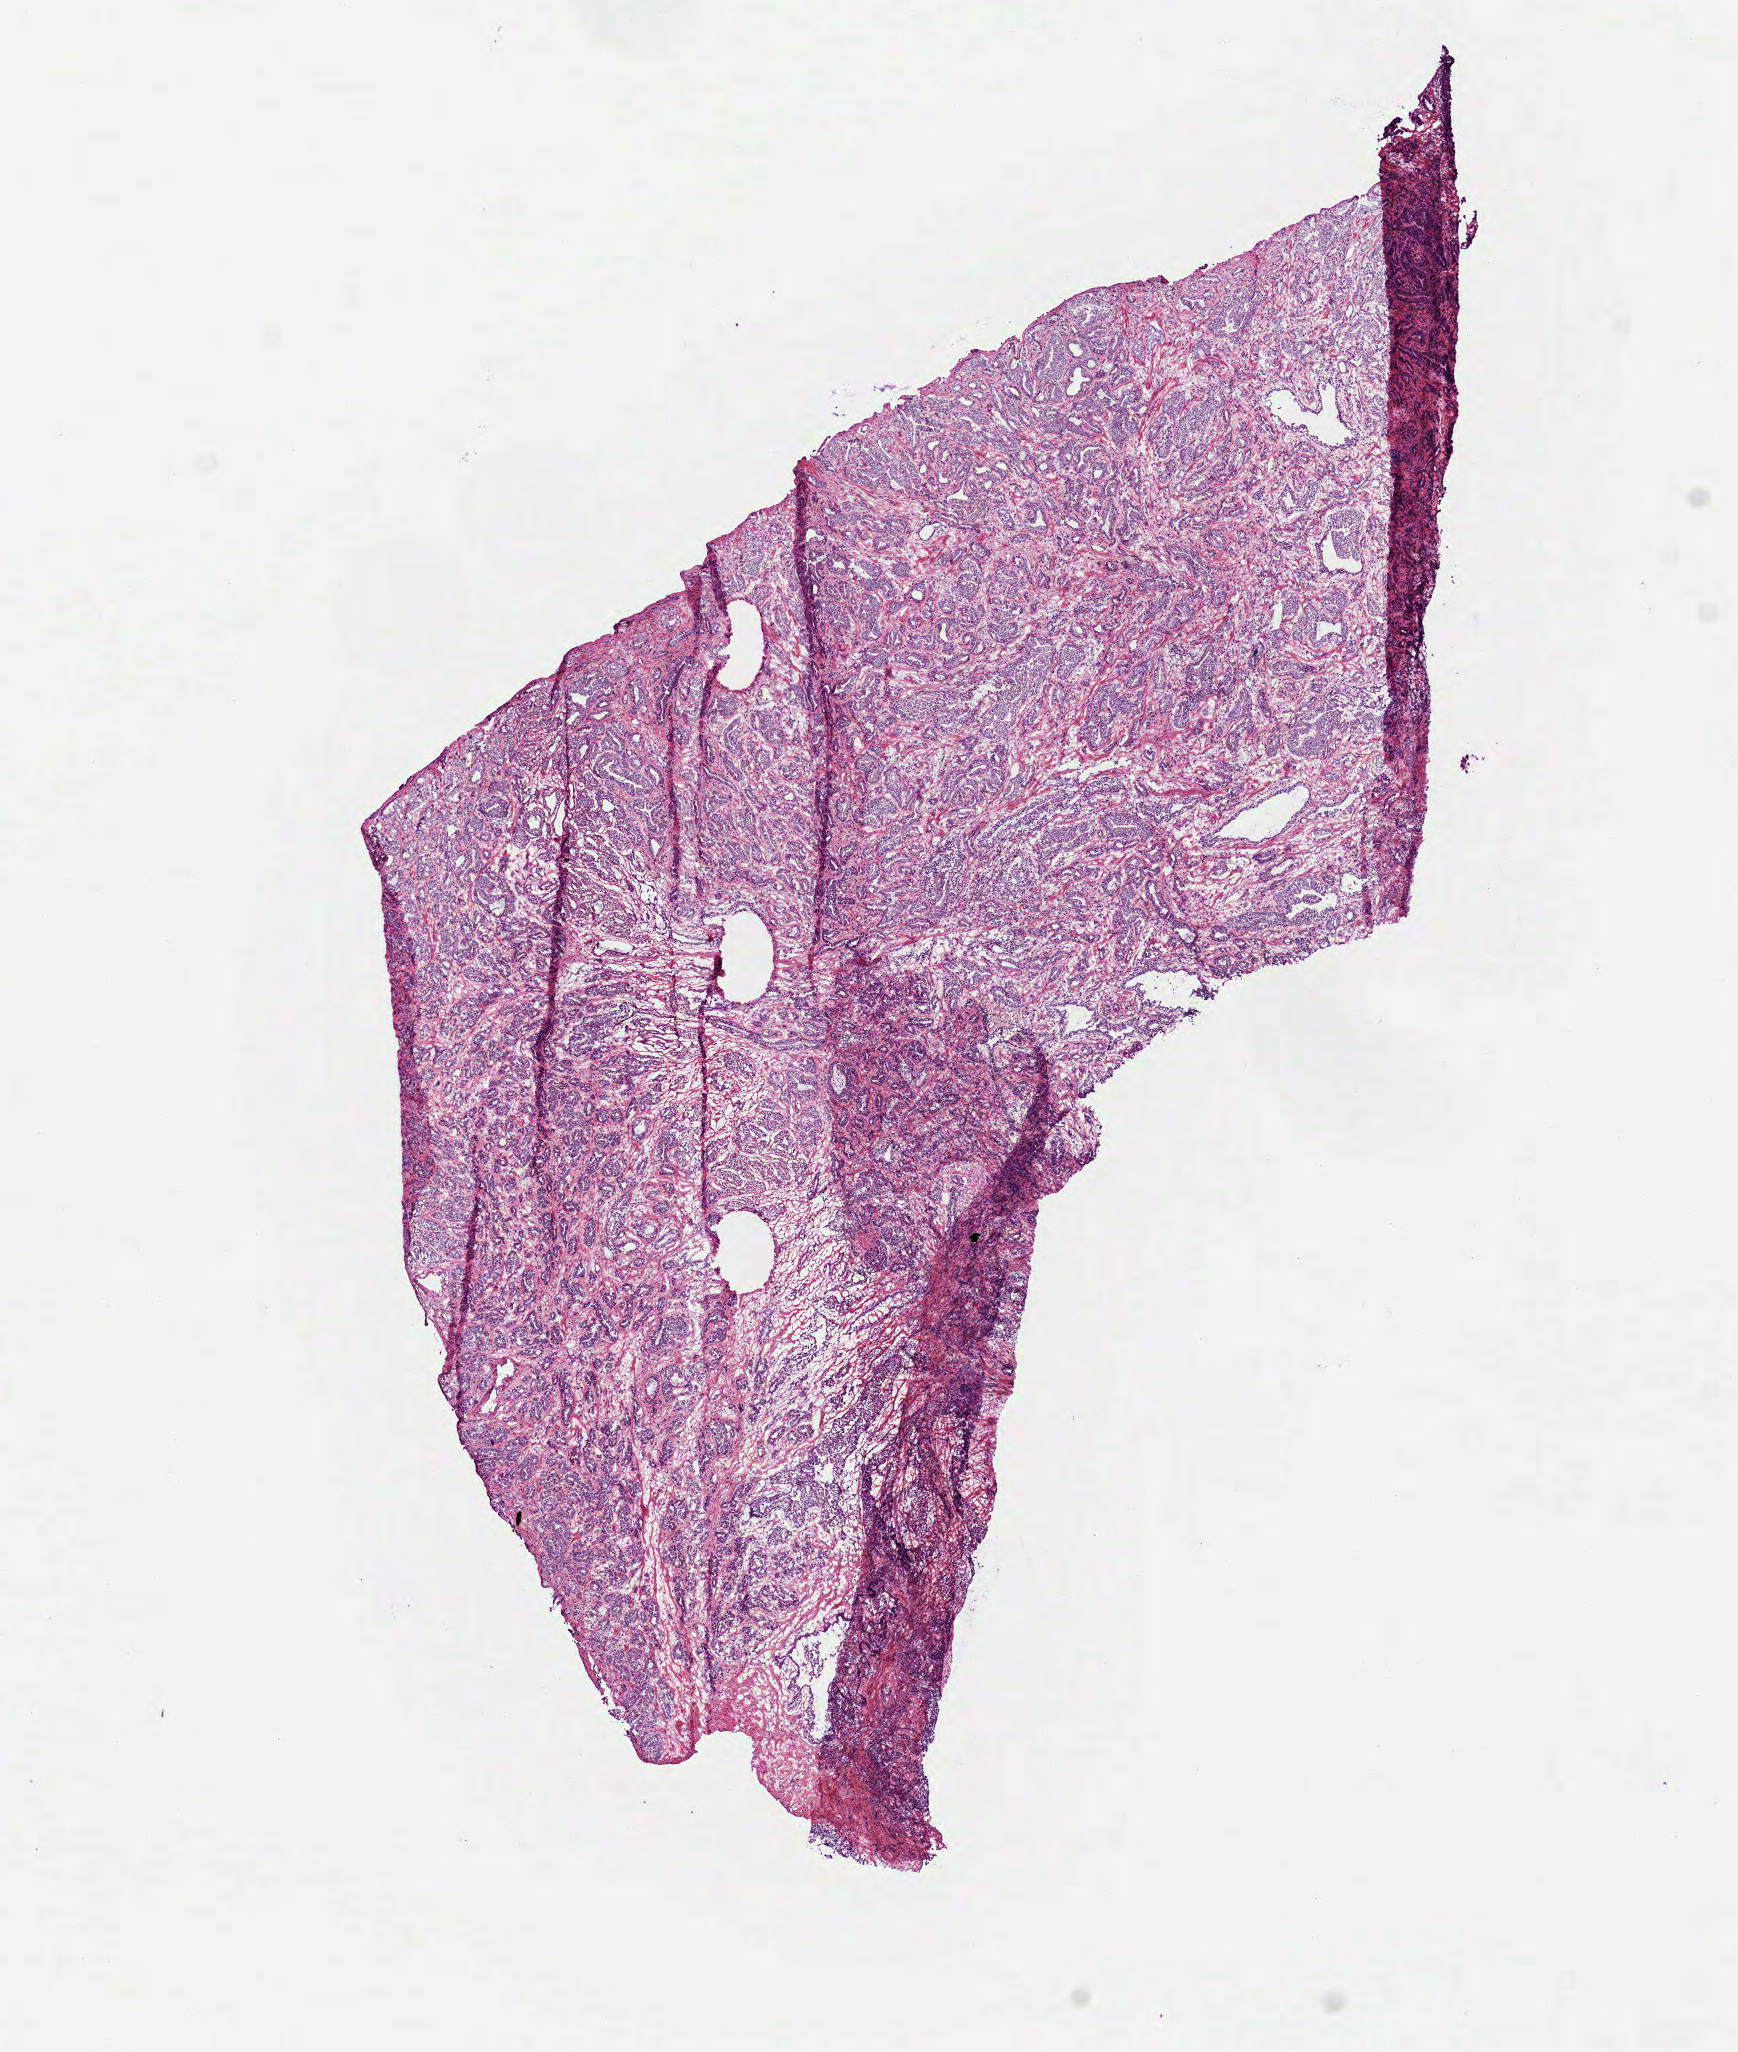
Digitized Hematoxylin and eosin (H&E) stained tissue section (whole slide), shown as a low-resolution overview of the whole scanned area (about 7.0 x 8.3 mm). Frozen section. Sample: primary tumour, prostate. Male patient; age at initial diagnosis 57 years. Gleason score: 6 (3+3). Pathologist review of this section (percent, as recorded): tumour nuclei 85%, necrosis 0%.
Pathologic diagnosis: Acinar cell carcinoma. Lymph nodes positive (case pathology): 0 of 25 examined.